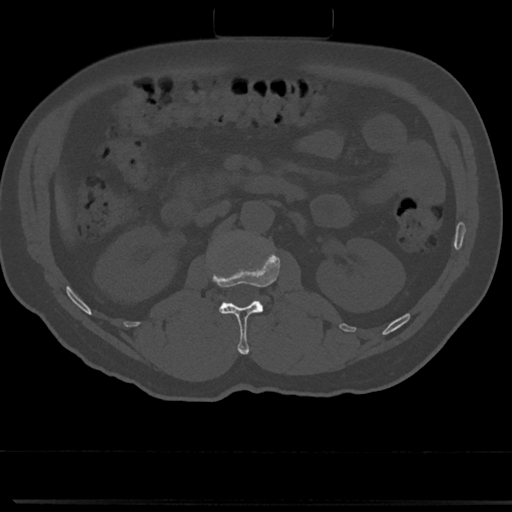
CT including the spine, one axial slice. Slice 62 of 817 in the series (ordered by position). Reconstruction kernel Br40s/3. Bone window (W 1800 / L 400 HU). 0.5 mm slice thickness. 512 × 512 image matrix, field of view 355 × 355 mm. Male patient, age 61 years. From the clinical record (not read from this slice): primary cancer: prostate.
Outlined on this slice (semi-automatic segmentation, software-assisted and operator-edited):
- L1 vertebra: bounding box (x1, y1, x2, y2) in pixels: (209, 252, 279, 354)